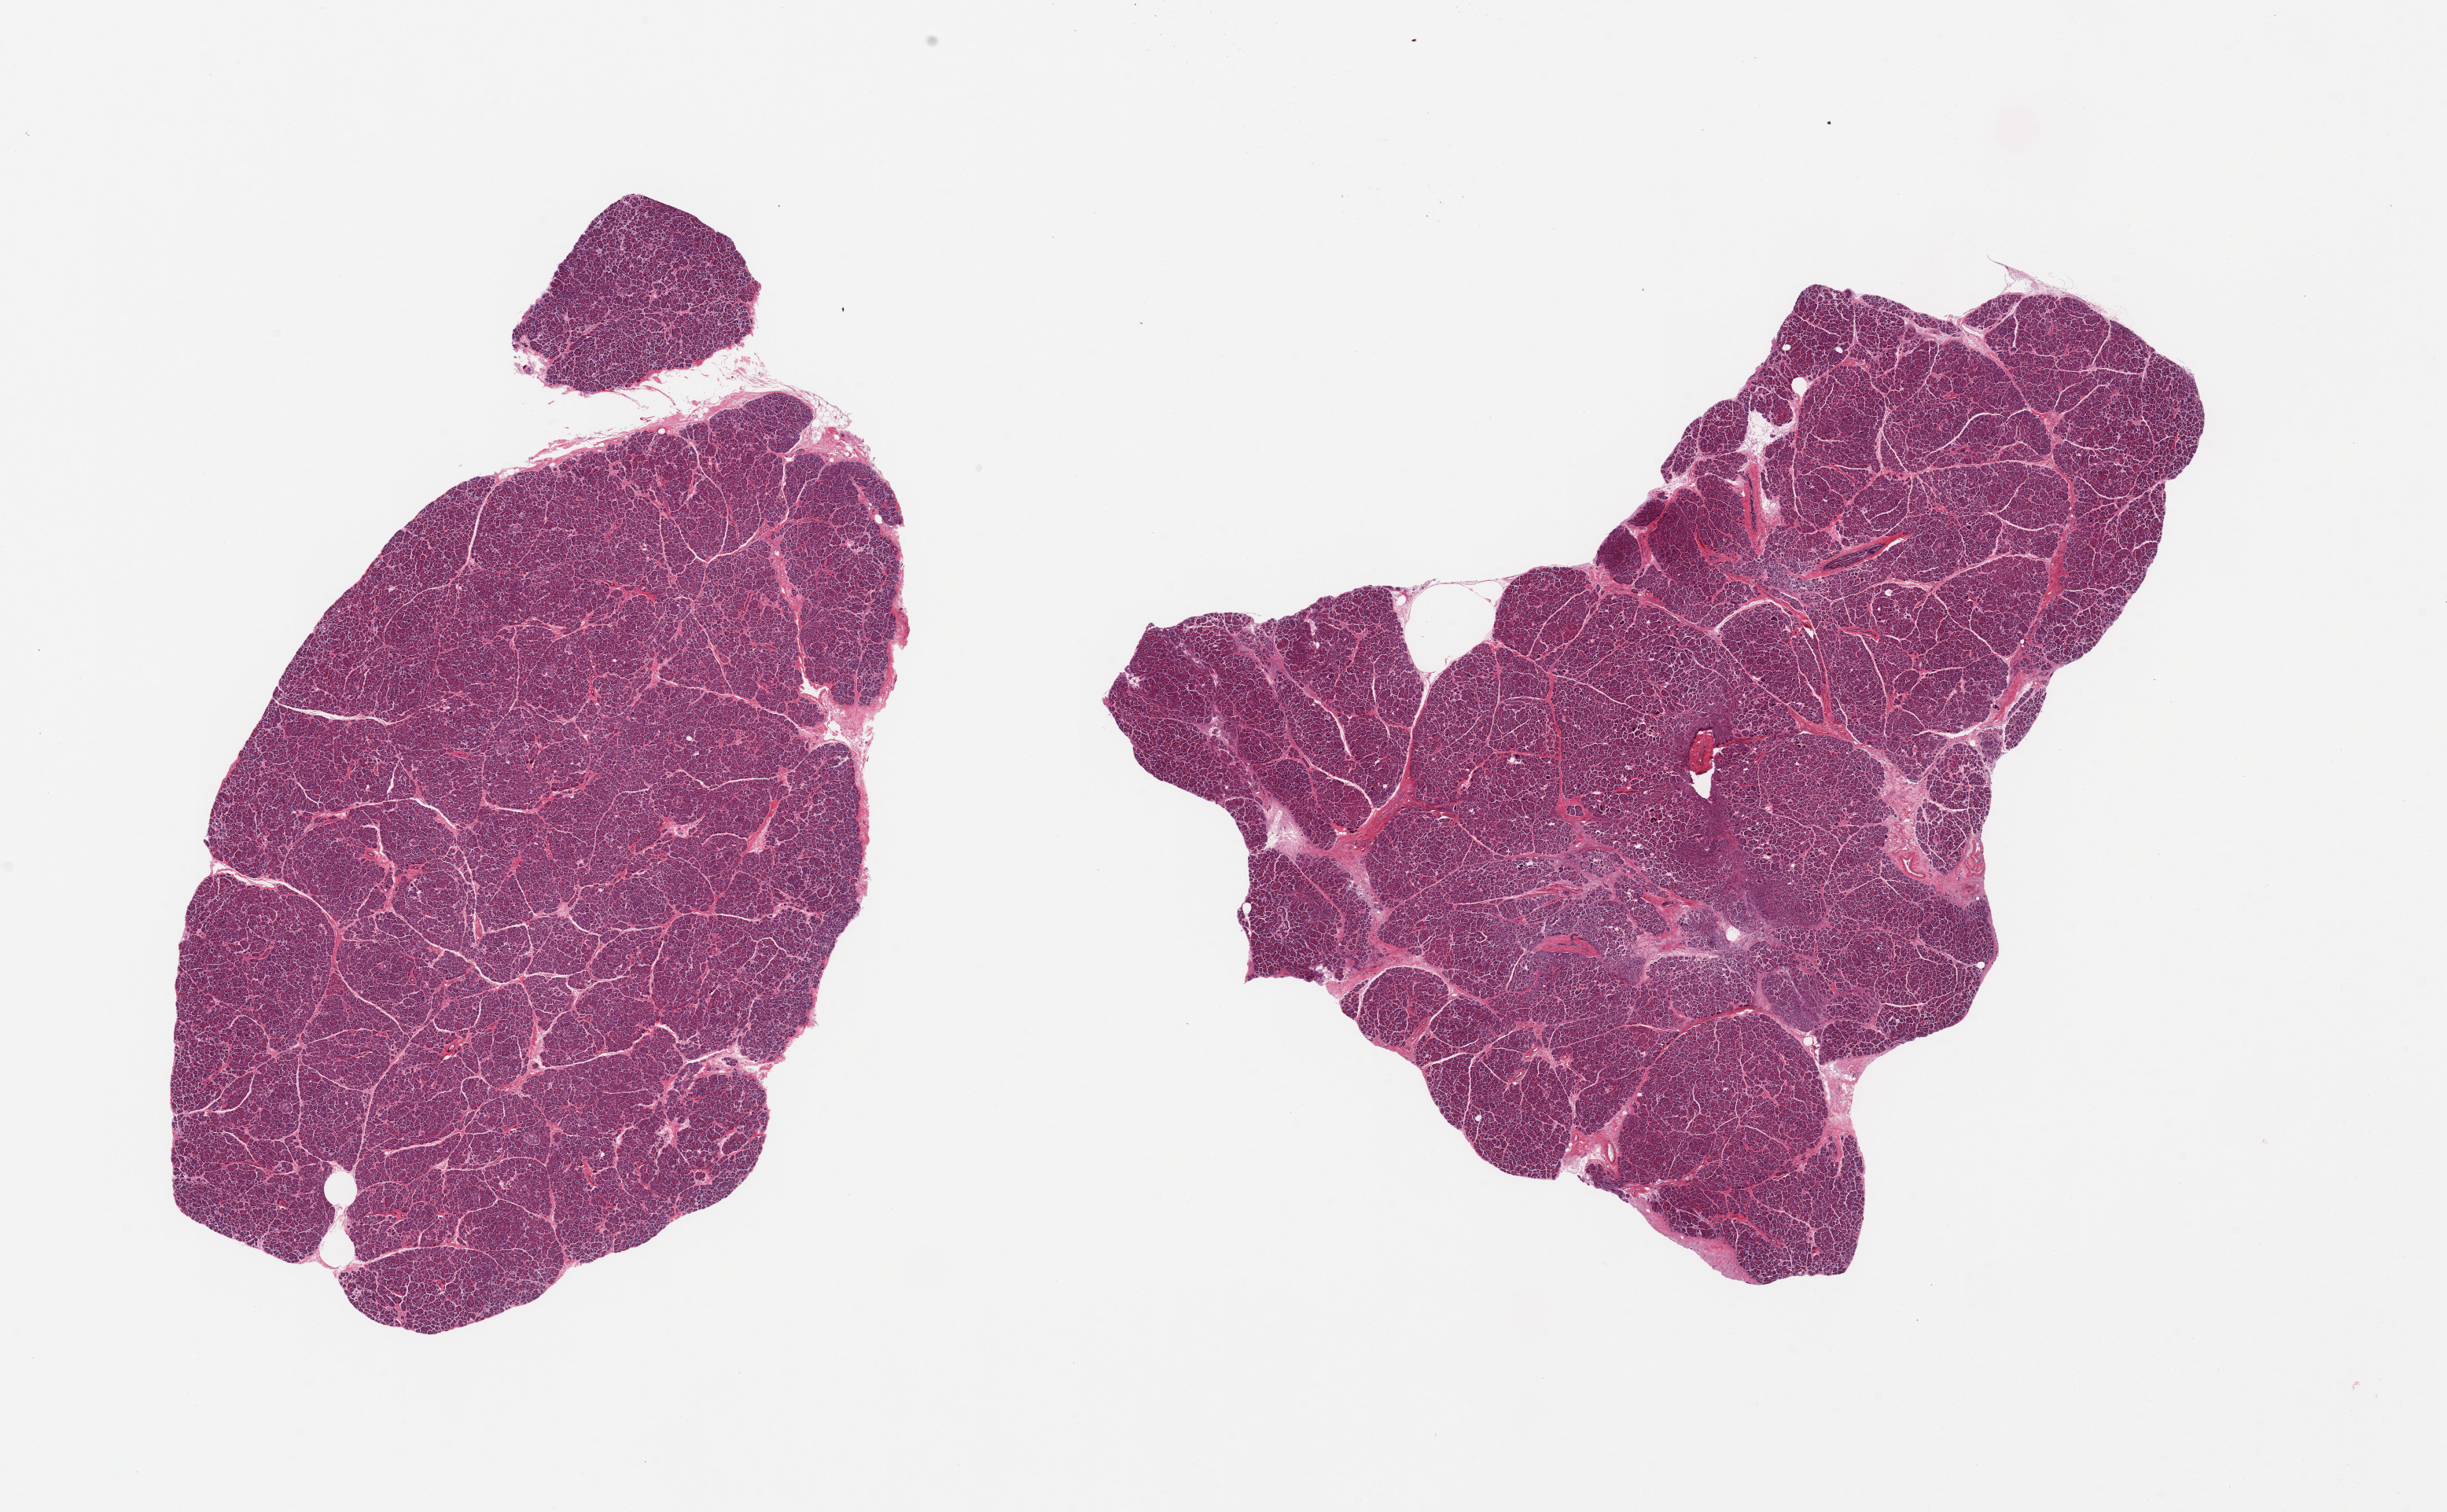
Hematoxylin and eosin (H&E) whole-slide image — a low-resolution overview of the entire scanned area, about 24.6 x 15.2 mm (slide scanned at 20x). PAXgene-fixed, paraffin-embedded tissue. Section of pancreas (target tissue). Donor tissue sample. Male donor.
Review note (as recorded): 2 pieces; rare foci of autolysis; <1% fat content.